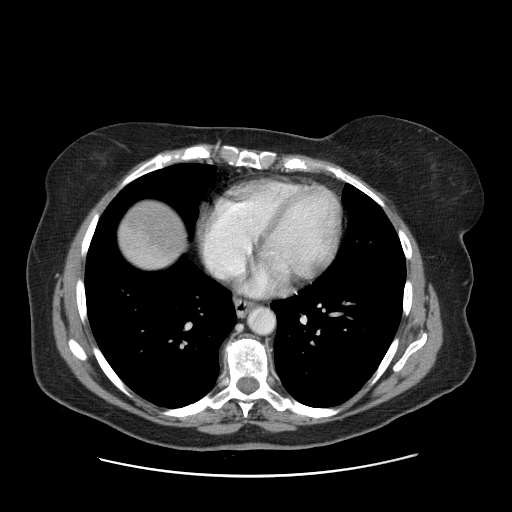
Contrast-enhanced abdominal CT, one axial slice. 120 kVp. Soft-tissue window (W 400 / L 40 HU). 2.5 mm slice thickness. 512 × 512 image matrix, field of view 398 × 398 mm. Female patient, age 62 years. Case-level facts recorded for this patient, not image findings: diagnosis: colorectal cancer liver metastases, imaged before liver resection; multiple liver metastases: no; largest metastasis: 2.5 cm.
Annotated regions visible in this slice (manually delineated by an expert):
- liver: bounding box (x1, y1, x2, y2) in pixels: (120, 202, 183, 268)
- planned liver remnant (the part of the liver to remain after resection): (119, 202, 183, 265)